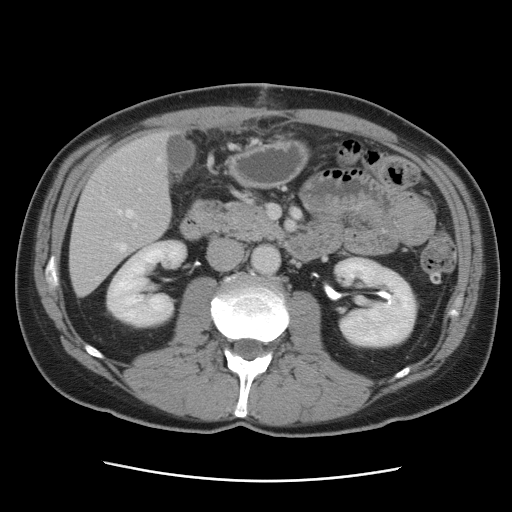
Contrast-enhanced abdominal CT, one axial slice; slice 34 of 89 in the series (ordered by position); 120 kVp; intravenous contrast given; soft-tissue window (W 400 / L 40 HU); 512 × 512 image matrix. Male patient, age 59 years. From the clinical record (not read from this slice): diagnosis: colorectal cancer liver metastases, imaged before liver resection; multiple liver metastases: yes; largest metastasis: 0.6 cm; disease in both lobes: yes.
Outlined on this slice (outlined manually by an expert reader):
- hepatic veins: bounding box [x1, y1, x2, y2] px = [96, 158, 162, 280]
- liver: [70, 132, 171, 296]
- planned liver remnant (the part of the liver to remain after resection): [74, 132, 171, 245]
- portal vein (with intrahepatic branches): [133, 189, 141, 228]